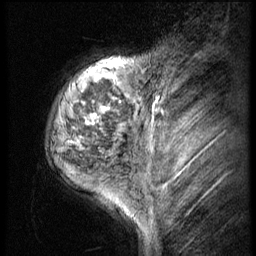
Breast MRI (dynamic contrast-enhanced), one sagittal slice; position 11 of 56 along the scan axis; 3 images stored at this slice position (order not interpretable as contrast timing); 1.5 T; TE 4.2 ms, TR 9 ms; 2.5 mm slice thickness; 256 × 256 image matrix. Female patient, age 50 years. Case-level facts recorded for this patient, not image findings: setting: breast cancer imaged before/during neoadjuvant chemotherapy; receptor status: triple-negative.
Annotated regions visible in this slice (semi-automatically segmented with operator editing):
- analysis volume of interest (the breast-tissue region the enhancement analysis was run in; not a lesion): bounding box <44,50,135,191> (left, top, right, bottom; pixels)
- tumour enhancement mask (voxels above the 140 % enhancement threshold inside the analysis volume of interest): <68,108,107,144>